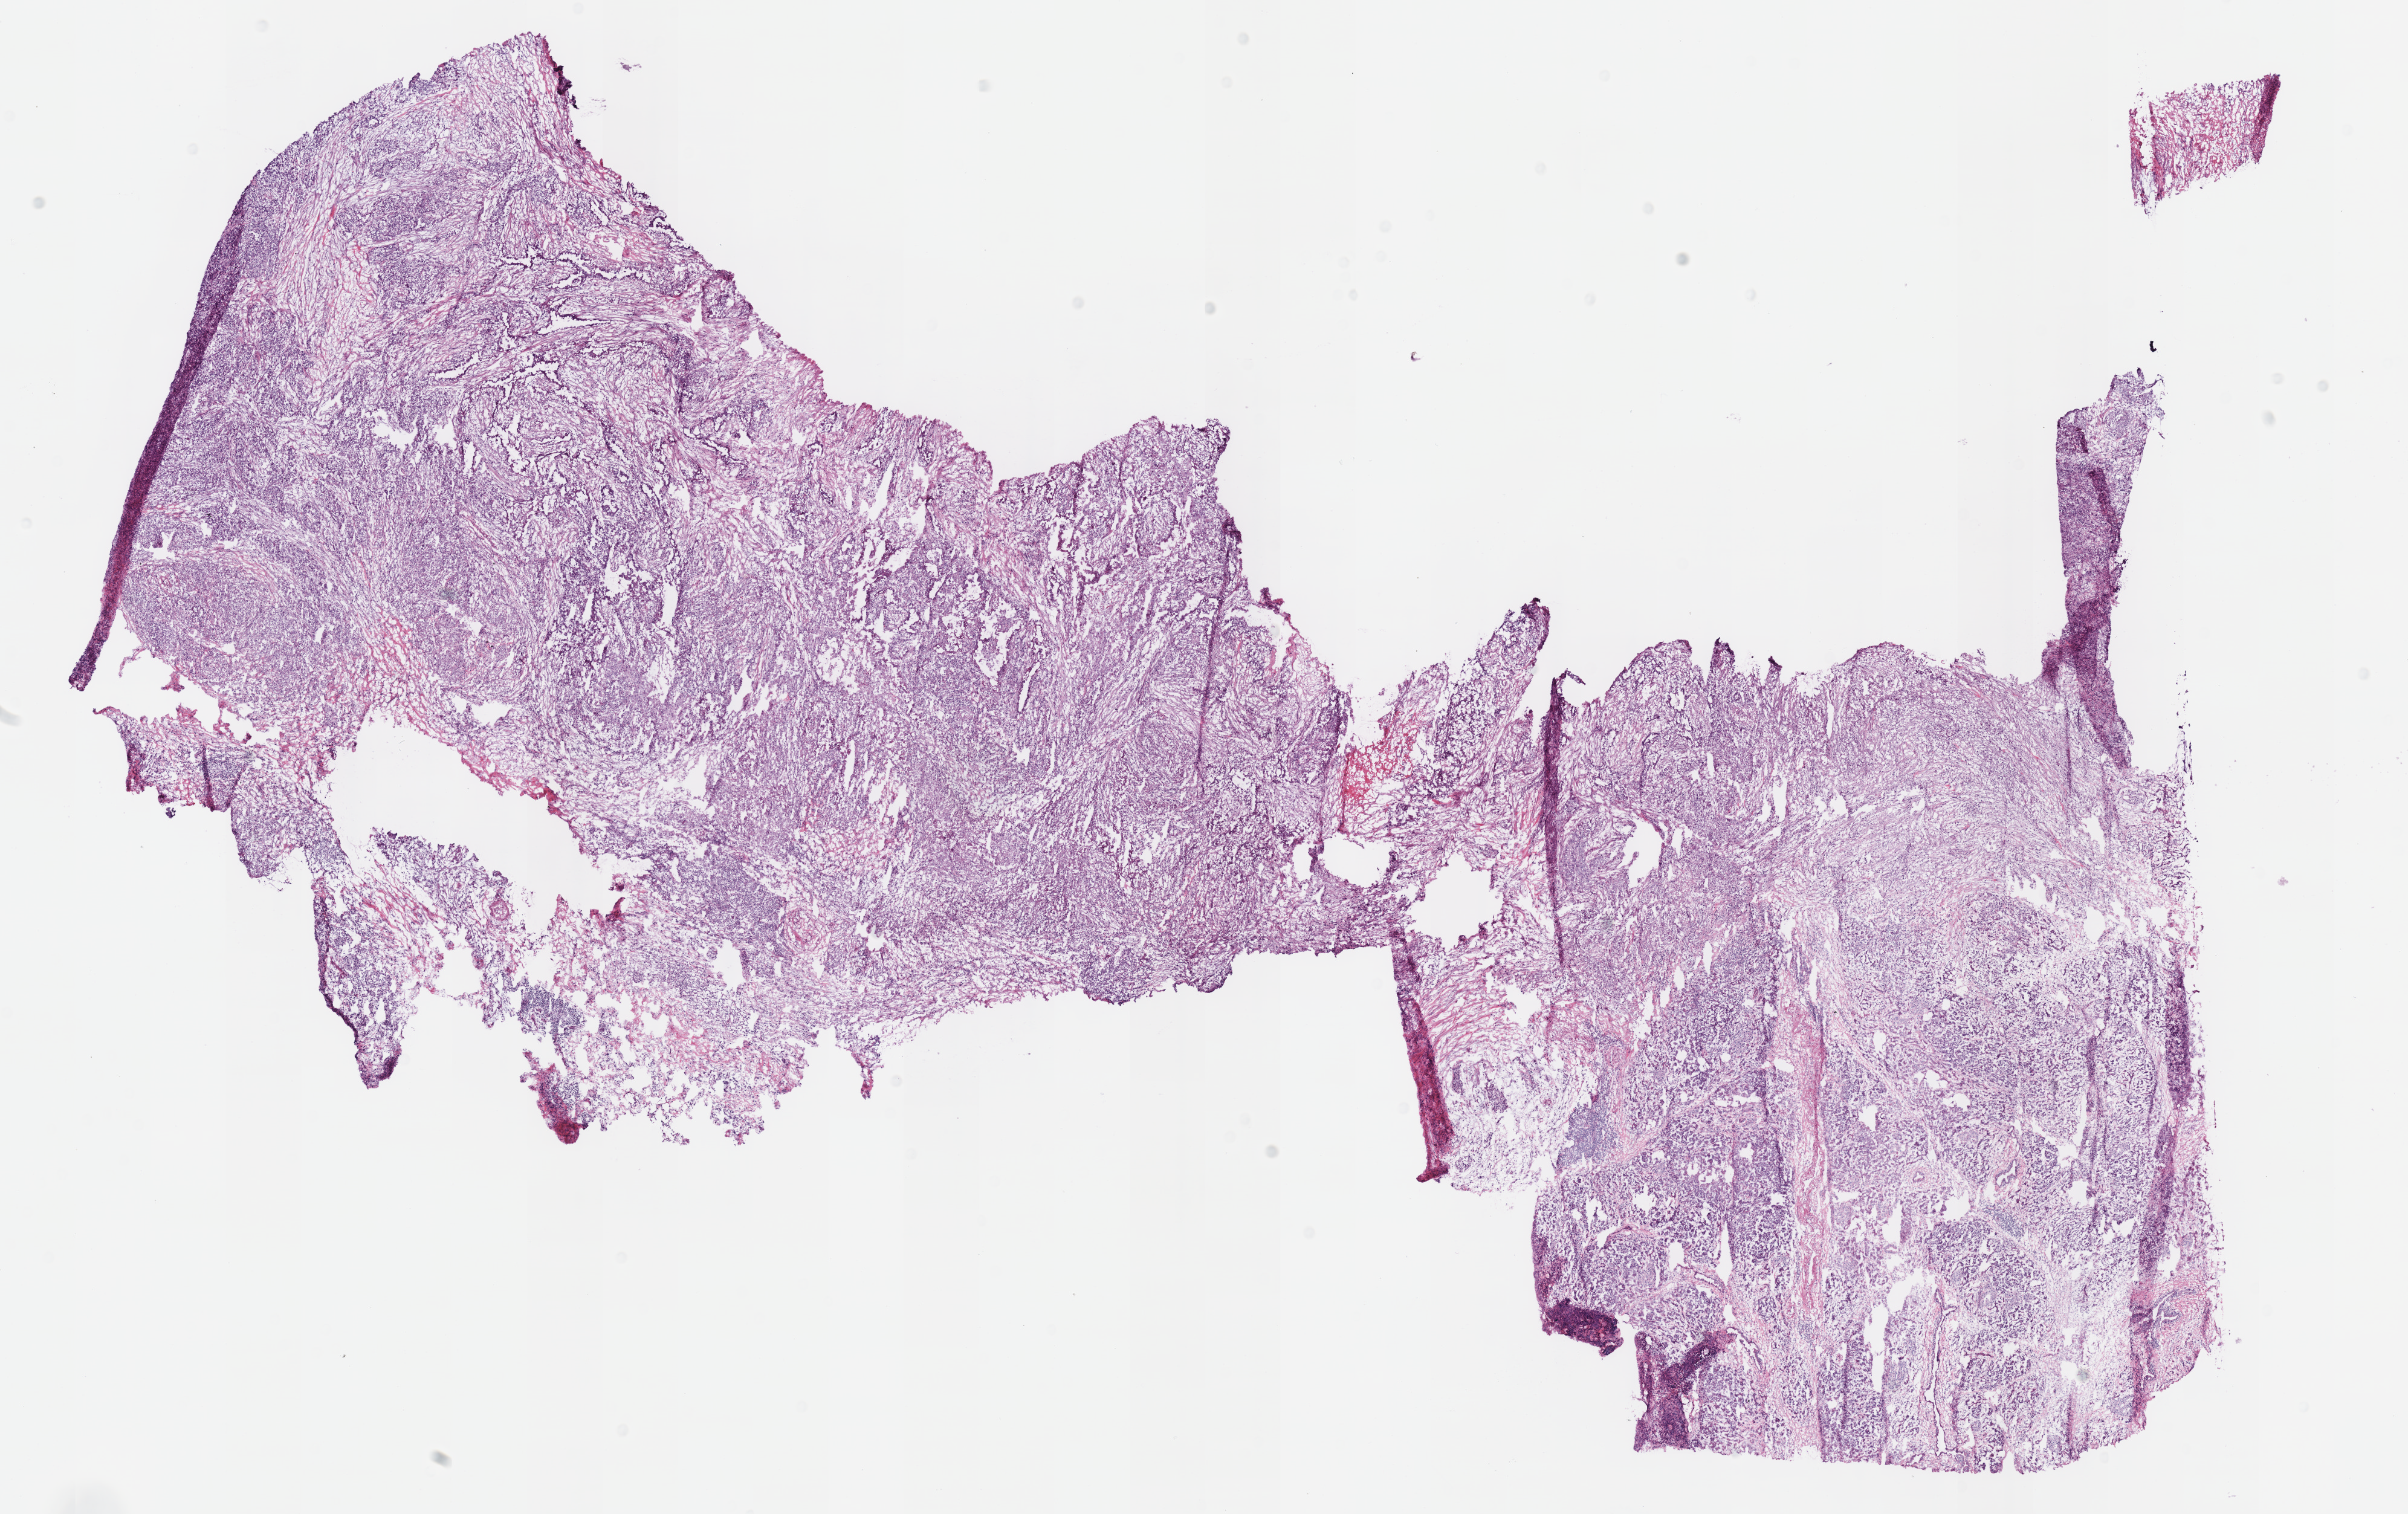
H&E-stained whole-slide image, low-resolution overview of the scanned area, about 15.7 x 9.8 mm (from a 40x scan), frozen section, primary tumour sample from the pancreas. Female patient; age at initial diagnosis 76 years. Histologic grade: G3 (poorly differentiated). Composition of this section per pathologist review: tumour cells 70%, tumour nuclei 55%, normal cells 20%, stromal cells 8%, necrosis 2%. Inflammatory infiltration, as recorded: lymphocyte infiltration 27%, monocyte infiltration 0%, neutrophil infiltration 0%.
AJCC pathologic stage: IIB (7th edition). Pathologic diagnosis: Infiltrating duct carcinoma, NOS (head of pancreas). Lymph nodes positive (case pathology): 1 of 18 examined. TNM: T3 N1 MX.